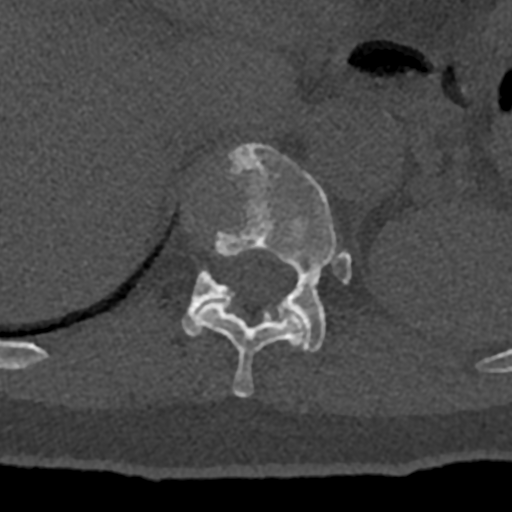
CT including the spine, one axial slice; position 520 of 797 along the scan axis; reconstruction kernel Br40s/3; bone window (W 1800 / L 400 HU); 512 × 512 image matrix, field of view 160 × 160 mm. Patient: male, 74 years. From the clinical record (not read from this slice): primary cancer: renal.
Structures marked on this image (semi-automatic segmentation, software-assisted and operator-edited):
- T11 vertebra: box from (x=193, y=301) to (x=307, y=398) px
- T12 vertebra: (x=182, y=142)–(x=351, y=352)